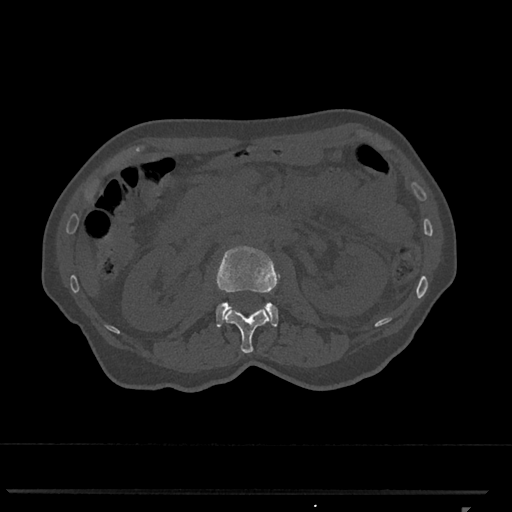
CT including the spine, one axial slice. Position 372 of 793 along the scan axis. Reconstruction kernel Br40s/3. Bone window (W 1800 / L 400 HU). 512 × 512 image matrix, field of view 380 × 380 mm. Patient: female, 62 years. From the clinical record (not read from this slice): primary cancer: renal.
Outlined on this slice (semi-automatically segmented with operator editing):
- L1 vertebra: bounding box (x1, y1, x2, y2) in pixels: (223, 306, 270, 354)
- L2 vertebra: (216, 246, 279, 327)